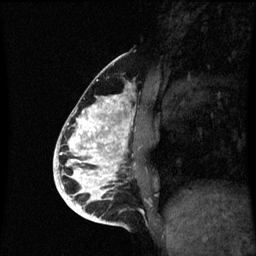
Breast MRI (dynamic contrast-enhanced), one sagittal slice. Slice 27 of 60 in the series (ordered by position). Dynamic contrast-enhanced series, image 2 of 3 at this slice position (ordered by acquisition). 1.5 T. TE 4.2 ms, TR 8.9 ms. 2 mm slice thickness. 256 × 256 image matrix, field of view 200 × 200 mm. Female patient, age 35 years. Case-level facts recorded for this patient, not image findings: setting: breast cancer imaged before/during neoadjuvant chemotherapy; receptor status: HR-positive, HER2-negative.
Structures marked on this image (semi-automatic segmentation, software-assisted and operator-edited):
- analysis volume of interest (the breast-tissue region the enhancement analysis was run in; not a lesion): bounding box <66,94,137,215> (left, top, right, bottom; pixels)
- tumour enhancement mask (voxels above the 70 % enhancement threshold inside the analysis volume of interest): <66,96,131,215>